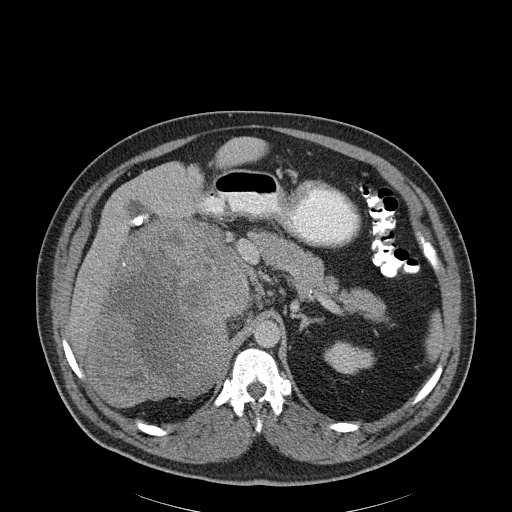
Contrast-enhanced abdominal CT, one axial slice; position 134 of 186 along the scan axis; 120 kVp; soft-tissue window (W 400 / L 40 HU); 3 mm slice thickness; 512 × 512 image matrix. Patient: male, 56 years. Case-level facts recorded for this patient, not image findings: diagnosis: adrenocortical carcinoma; tumour side: right adrenal; tumour size at pathology: 18 cm; Ki-67 index: 2 %; stage (as recorded): 3.
Annotated regions visible in this slice (semi-automatically segmented with operator editing):
- mass: box from (x=87, y=222) to (x=246, y=408) px